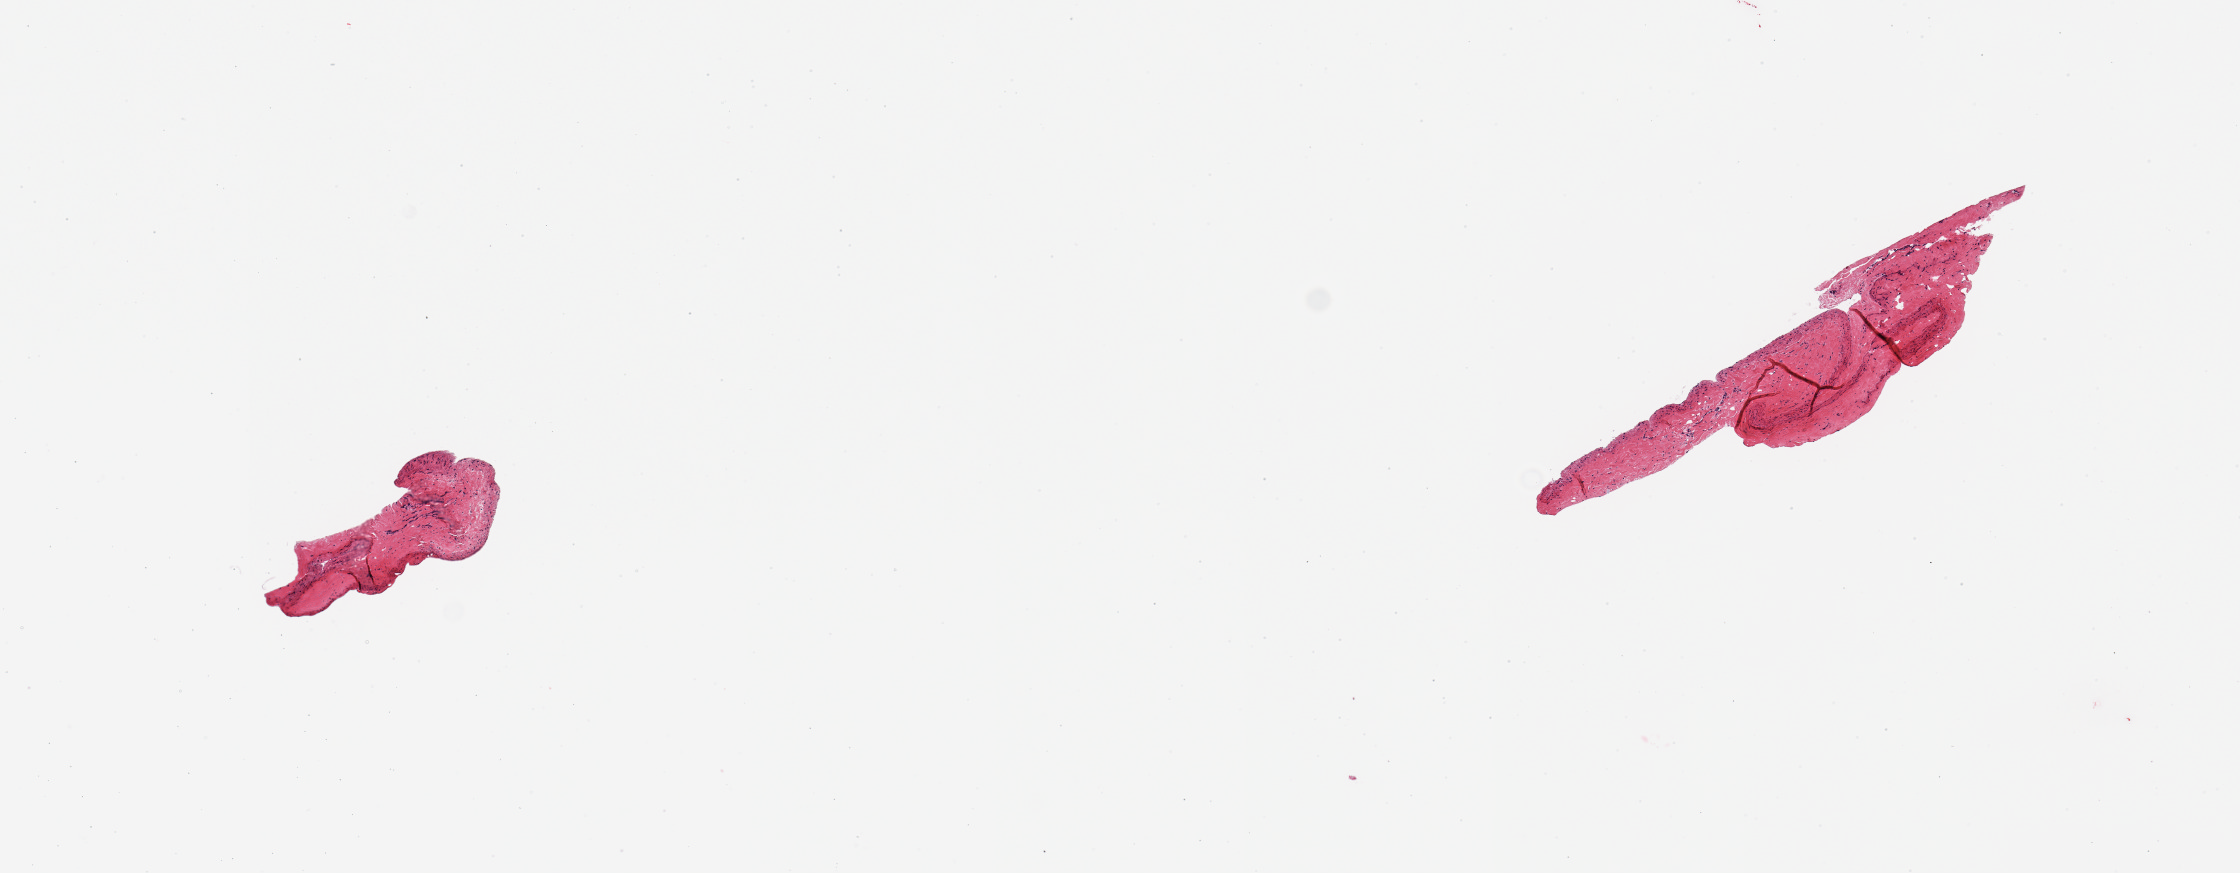
Whole-slide image, H&E stain, low-resolution overview of the scanned area, about 8.9 x 3.5 mm (slide scanned at 20x). PAXgene-fixed paraffin-embedded (PFPE) section. Sampled site (target tissue): coronary artery. Donor tissue sample. Donor sex: male.
Reviewer comment on this tissue sample: 2 pieces; vein rather than artery.